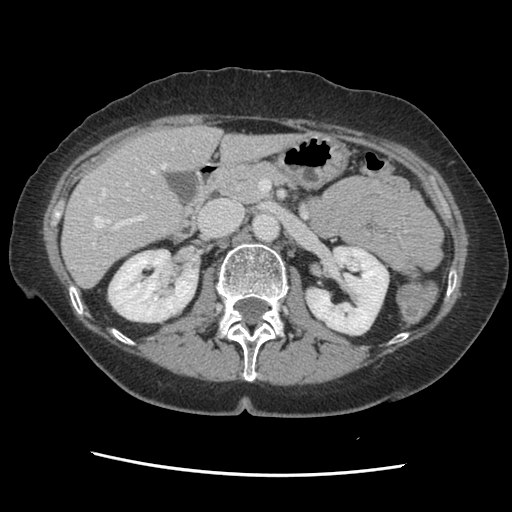
Contrast-enhanced abdominal CT, one axial slice; slice 71 of 141 in the series (ordered by position); soft-tissue window (W 400 / L 40 HU); 512 × 512 image matrix, field of view 330 × 330 mm. Female patient, age 61 years. Case-level facts recorded for this patient, not image findings: diagnosis: colorectal cancer liver metastases, imaged before liver resection; multiple liver metastases: no; largest metastasis: 2.4 cm.
Annotated regions visible in this slice (outlined manually by an expert reader):
- hepatic veins: bounding box <88,149,173,228> (left, top, right, bottom; pixels)
- liver: <63,126,295,287>
- planned liver remnant (the part of the liver to remain after resection): <63,127,295,287>
- portal vein (with intrahepatic branches): <92,183,146,246>